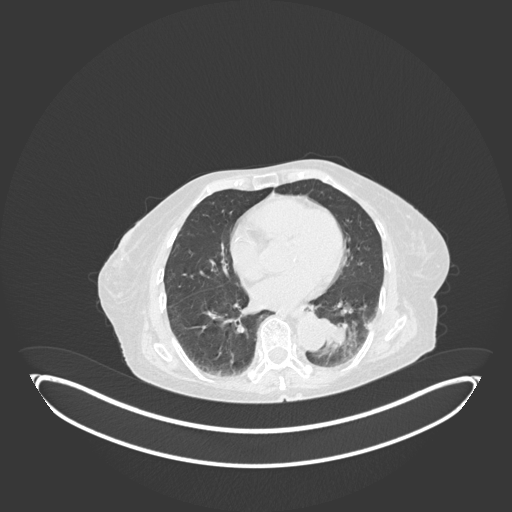
Chest CT, one axial slice. Position 42 of 189 along the scan axis. Reconstruction kernel B30f. 120 kVp. Lung window (W 1500 / L -600 HU). 1 mm slice thickness. 512 × 512 image matrix. Patient: female, 82 years. Case-level facts recorded for this patient, not image findings: clinical TNM (as recorded): T1b N0 M1.
Annotated regions visible in this slice (bounding box drawn by a radiologist):
- lung tumour (recorded histology: adenocarcinoma): bounding box <320,311,361,350> (left, top, right, bottom; pixels)